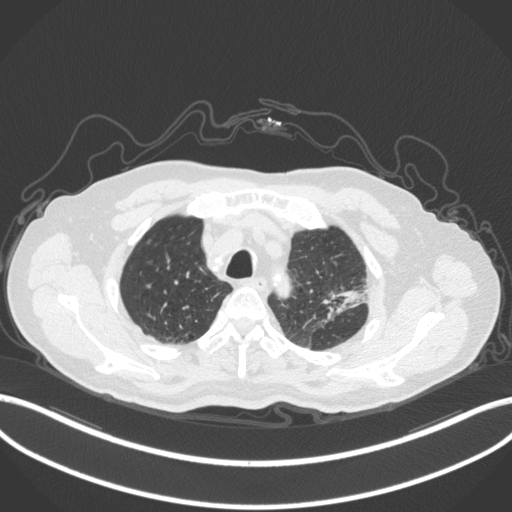
Chest CT, one axial slice. Reconstruction kernel B31f. Lung window (W 1500 / L -600 HU). 1 mm slice thickness. 512 × 512 image matrix. Male patient, age 79 years. From the clinical record (not read from this slice): clinical TNM (as recorded): T2a N1 M1.
Structures marked on this image (bounding box drawn by a radiologist):
- lung tumour (recorded histology: adenocarcinoma): bounding box <320,286,370,316> (left, top, right, bottom; pixels)